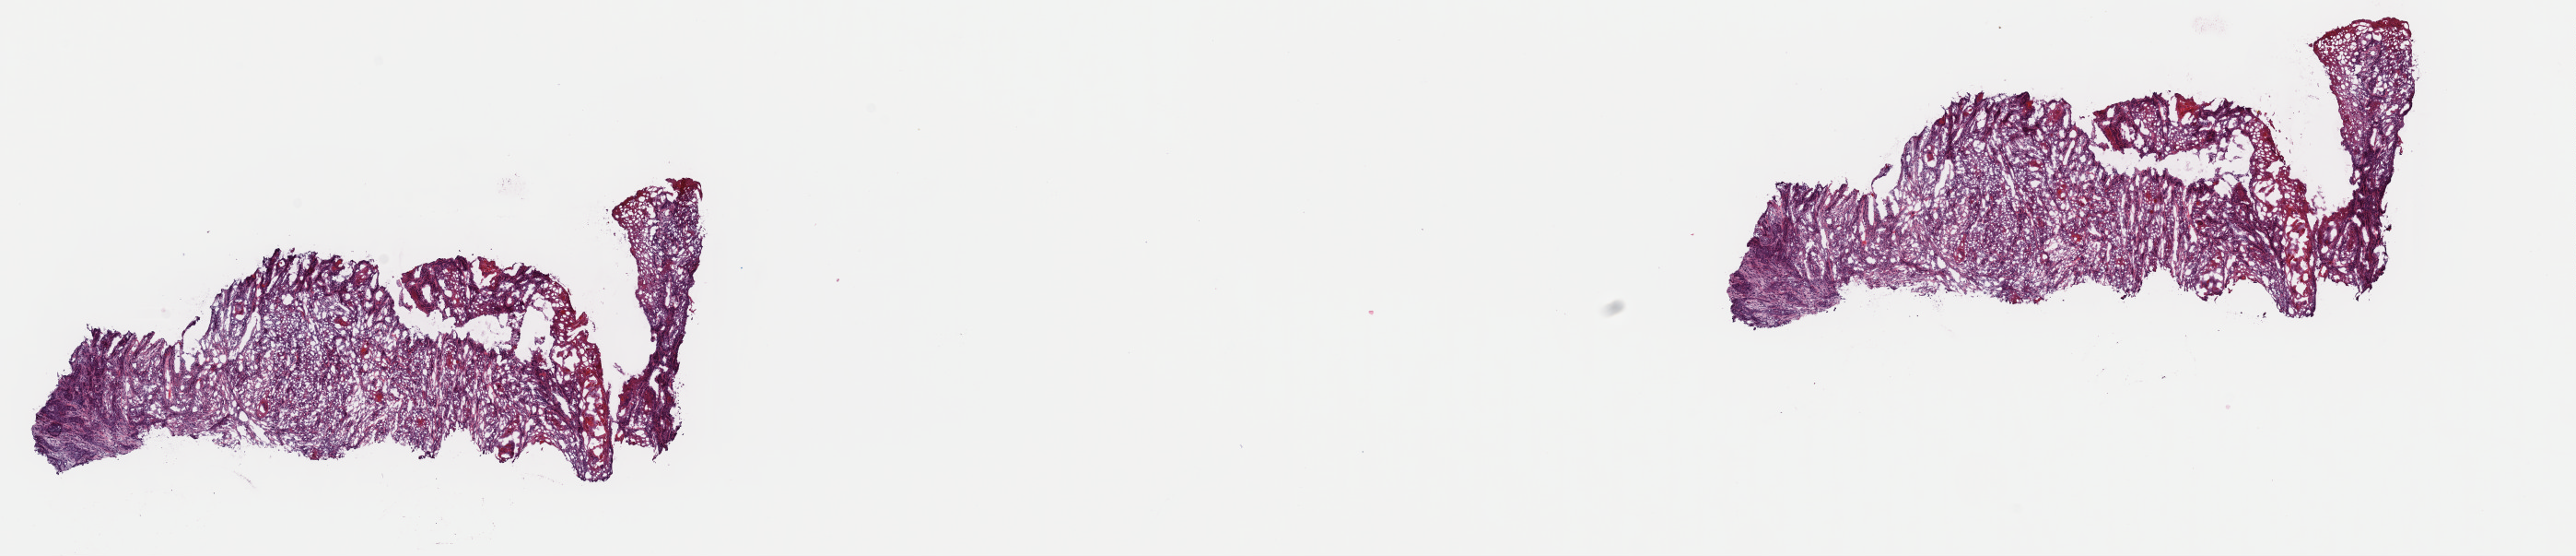
H&E-stained whole-slide image, whole scanned area (about 22.1 x 4.8 mm, acquisition: 40x scan) shown as a low-resolution overview, frozen section, sample: primary tumour, head and neck. Patient: female, age at initial diagnosis 55 years.
Pathologic diagnosis: Squamous cell carcinoma, NOS.